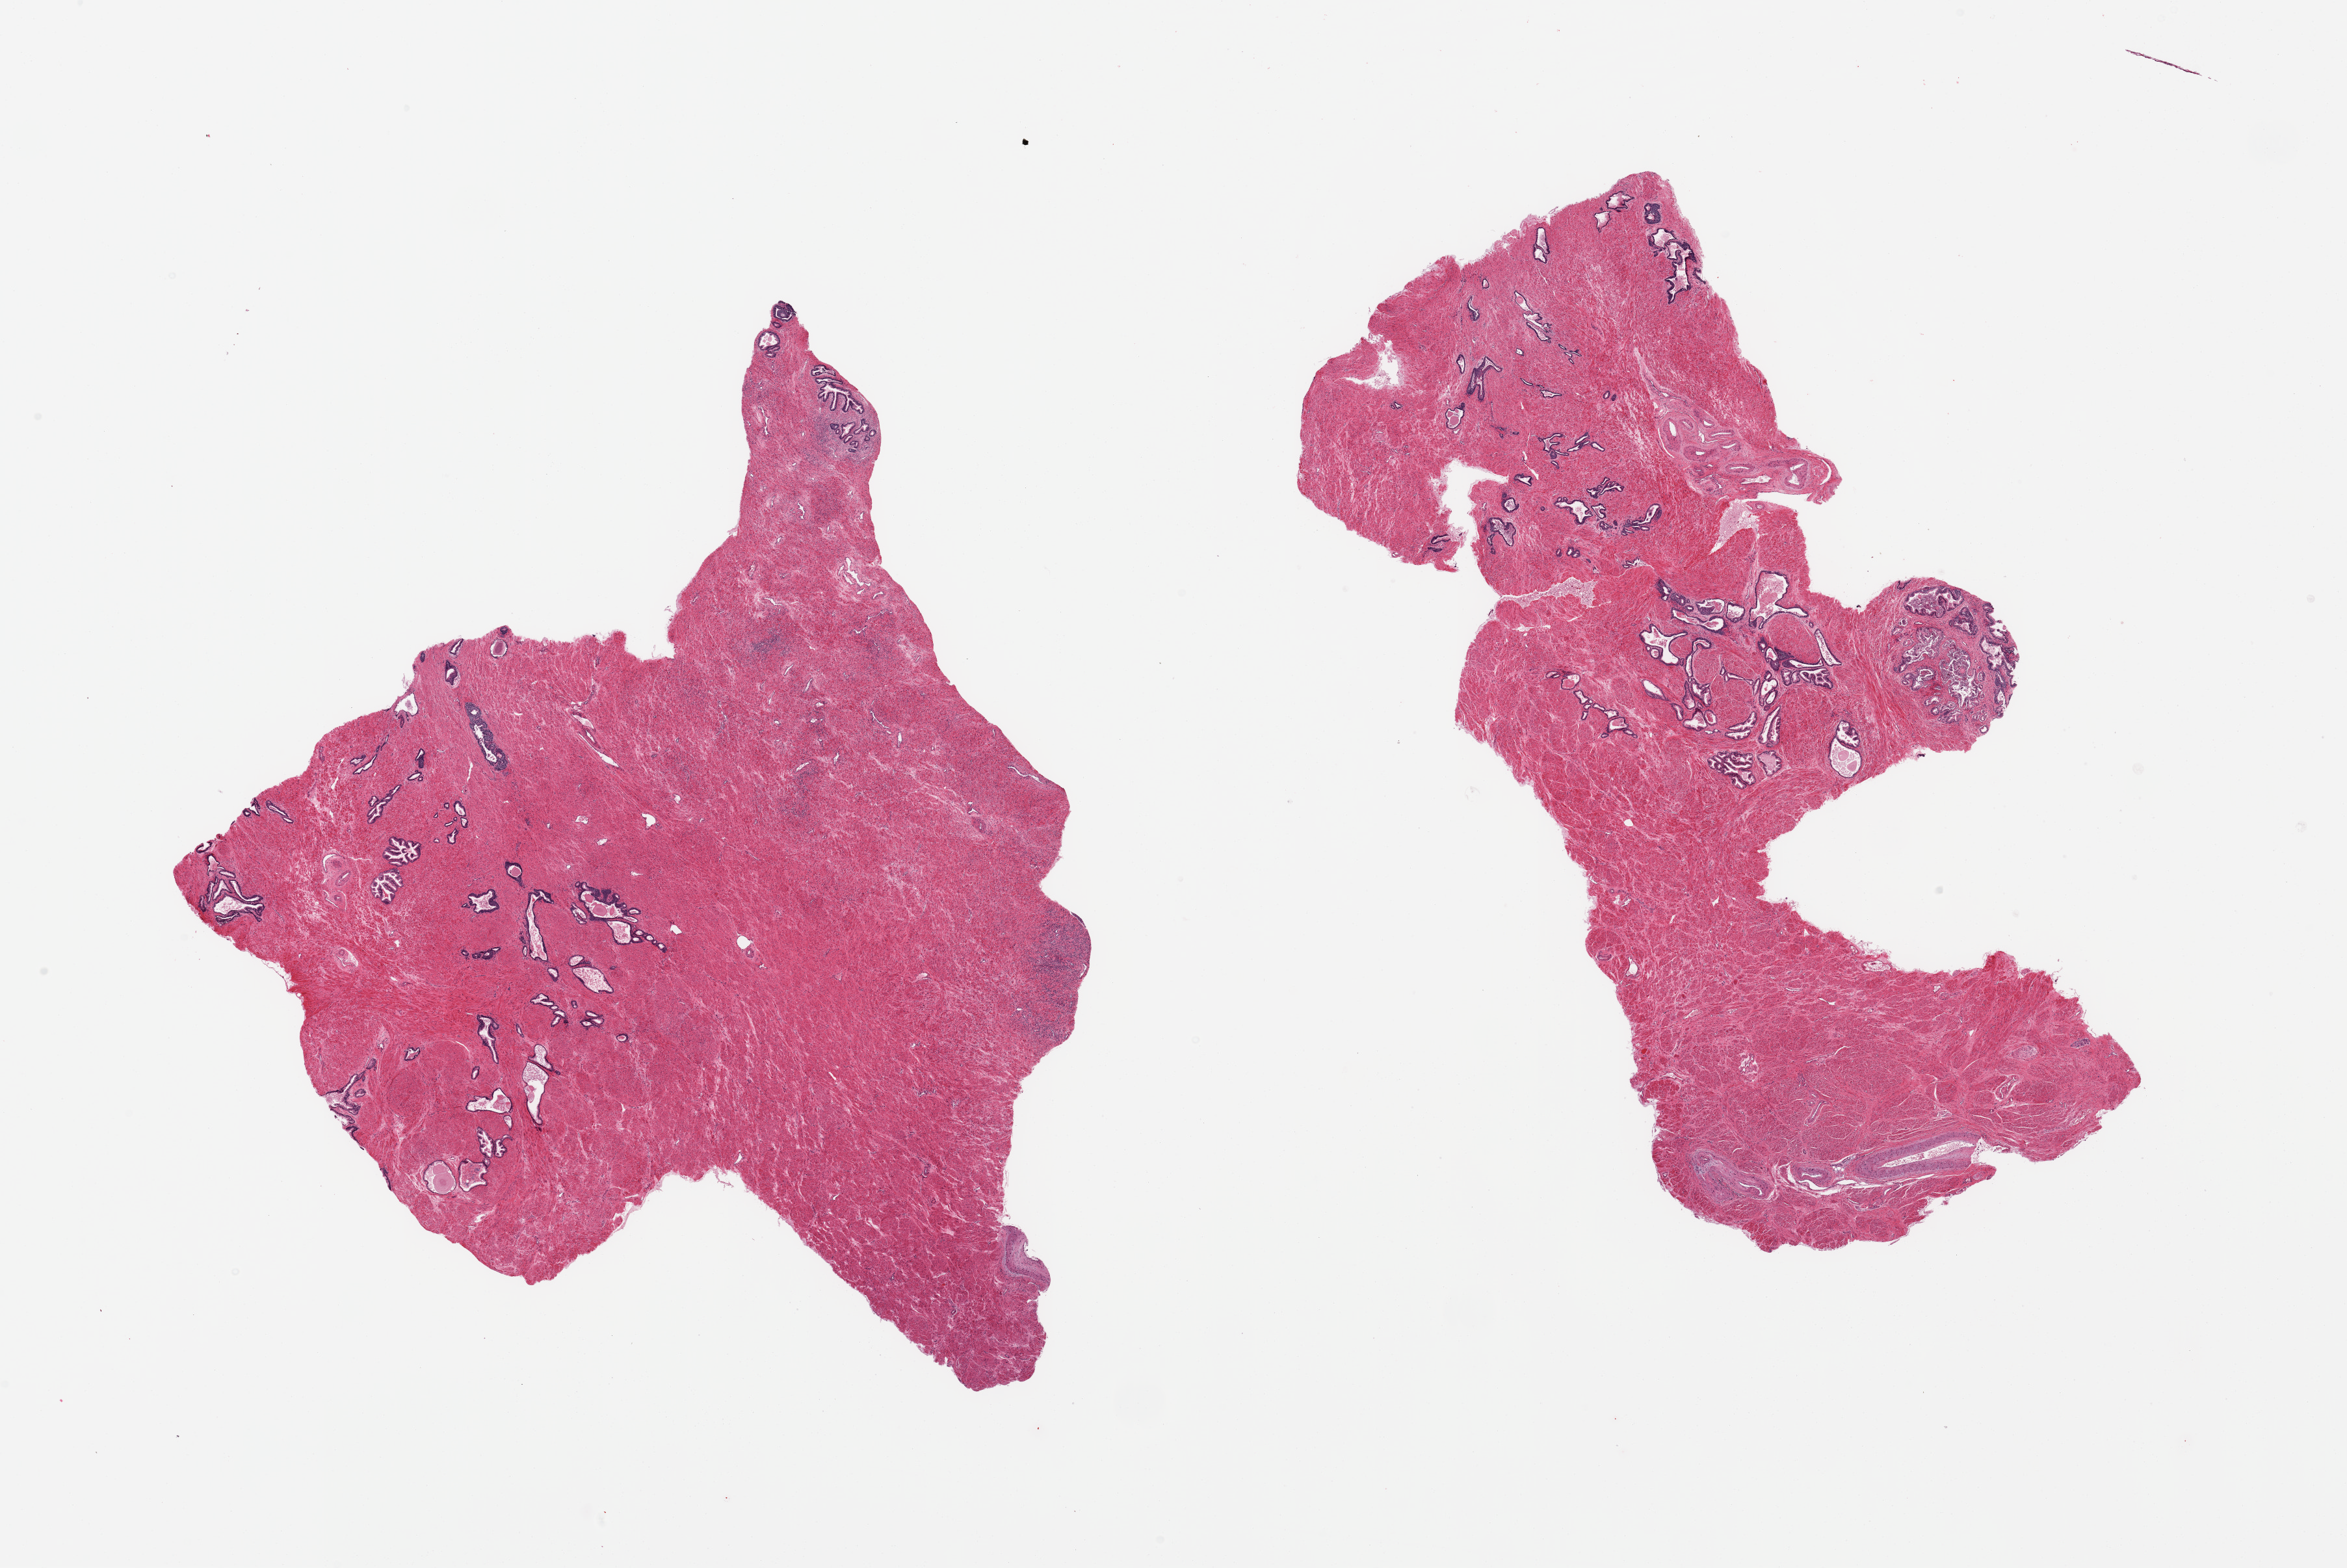
Whole-slide image, H&E stain, low-resolution overview of the scanned area, about 28.5 x 19.1 mm (acquisition: 20x scan). PAXgene-fixed, paraffin-embedded tissue. Sampled site (target tissue): prostate. Tissue donor sample. Male donor.
Pathologist's review note for this sample: 2 pieces, mild gland hyperplastic pattern.